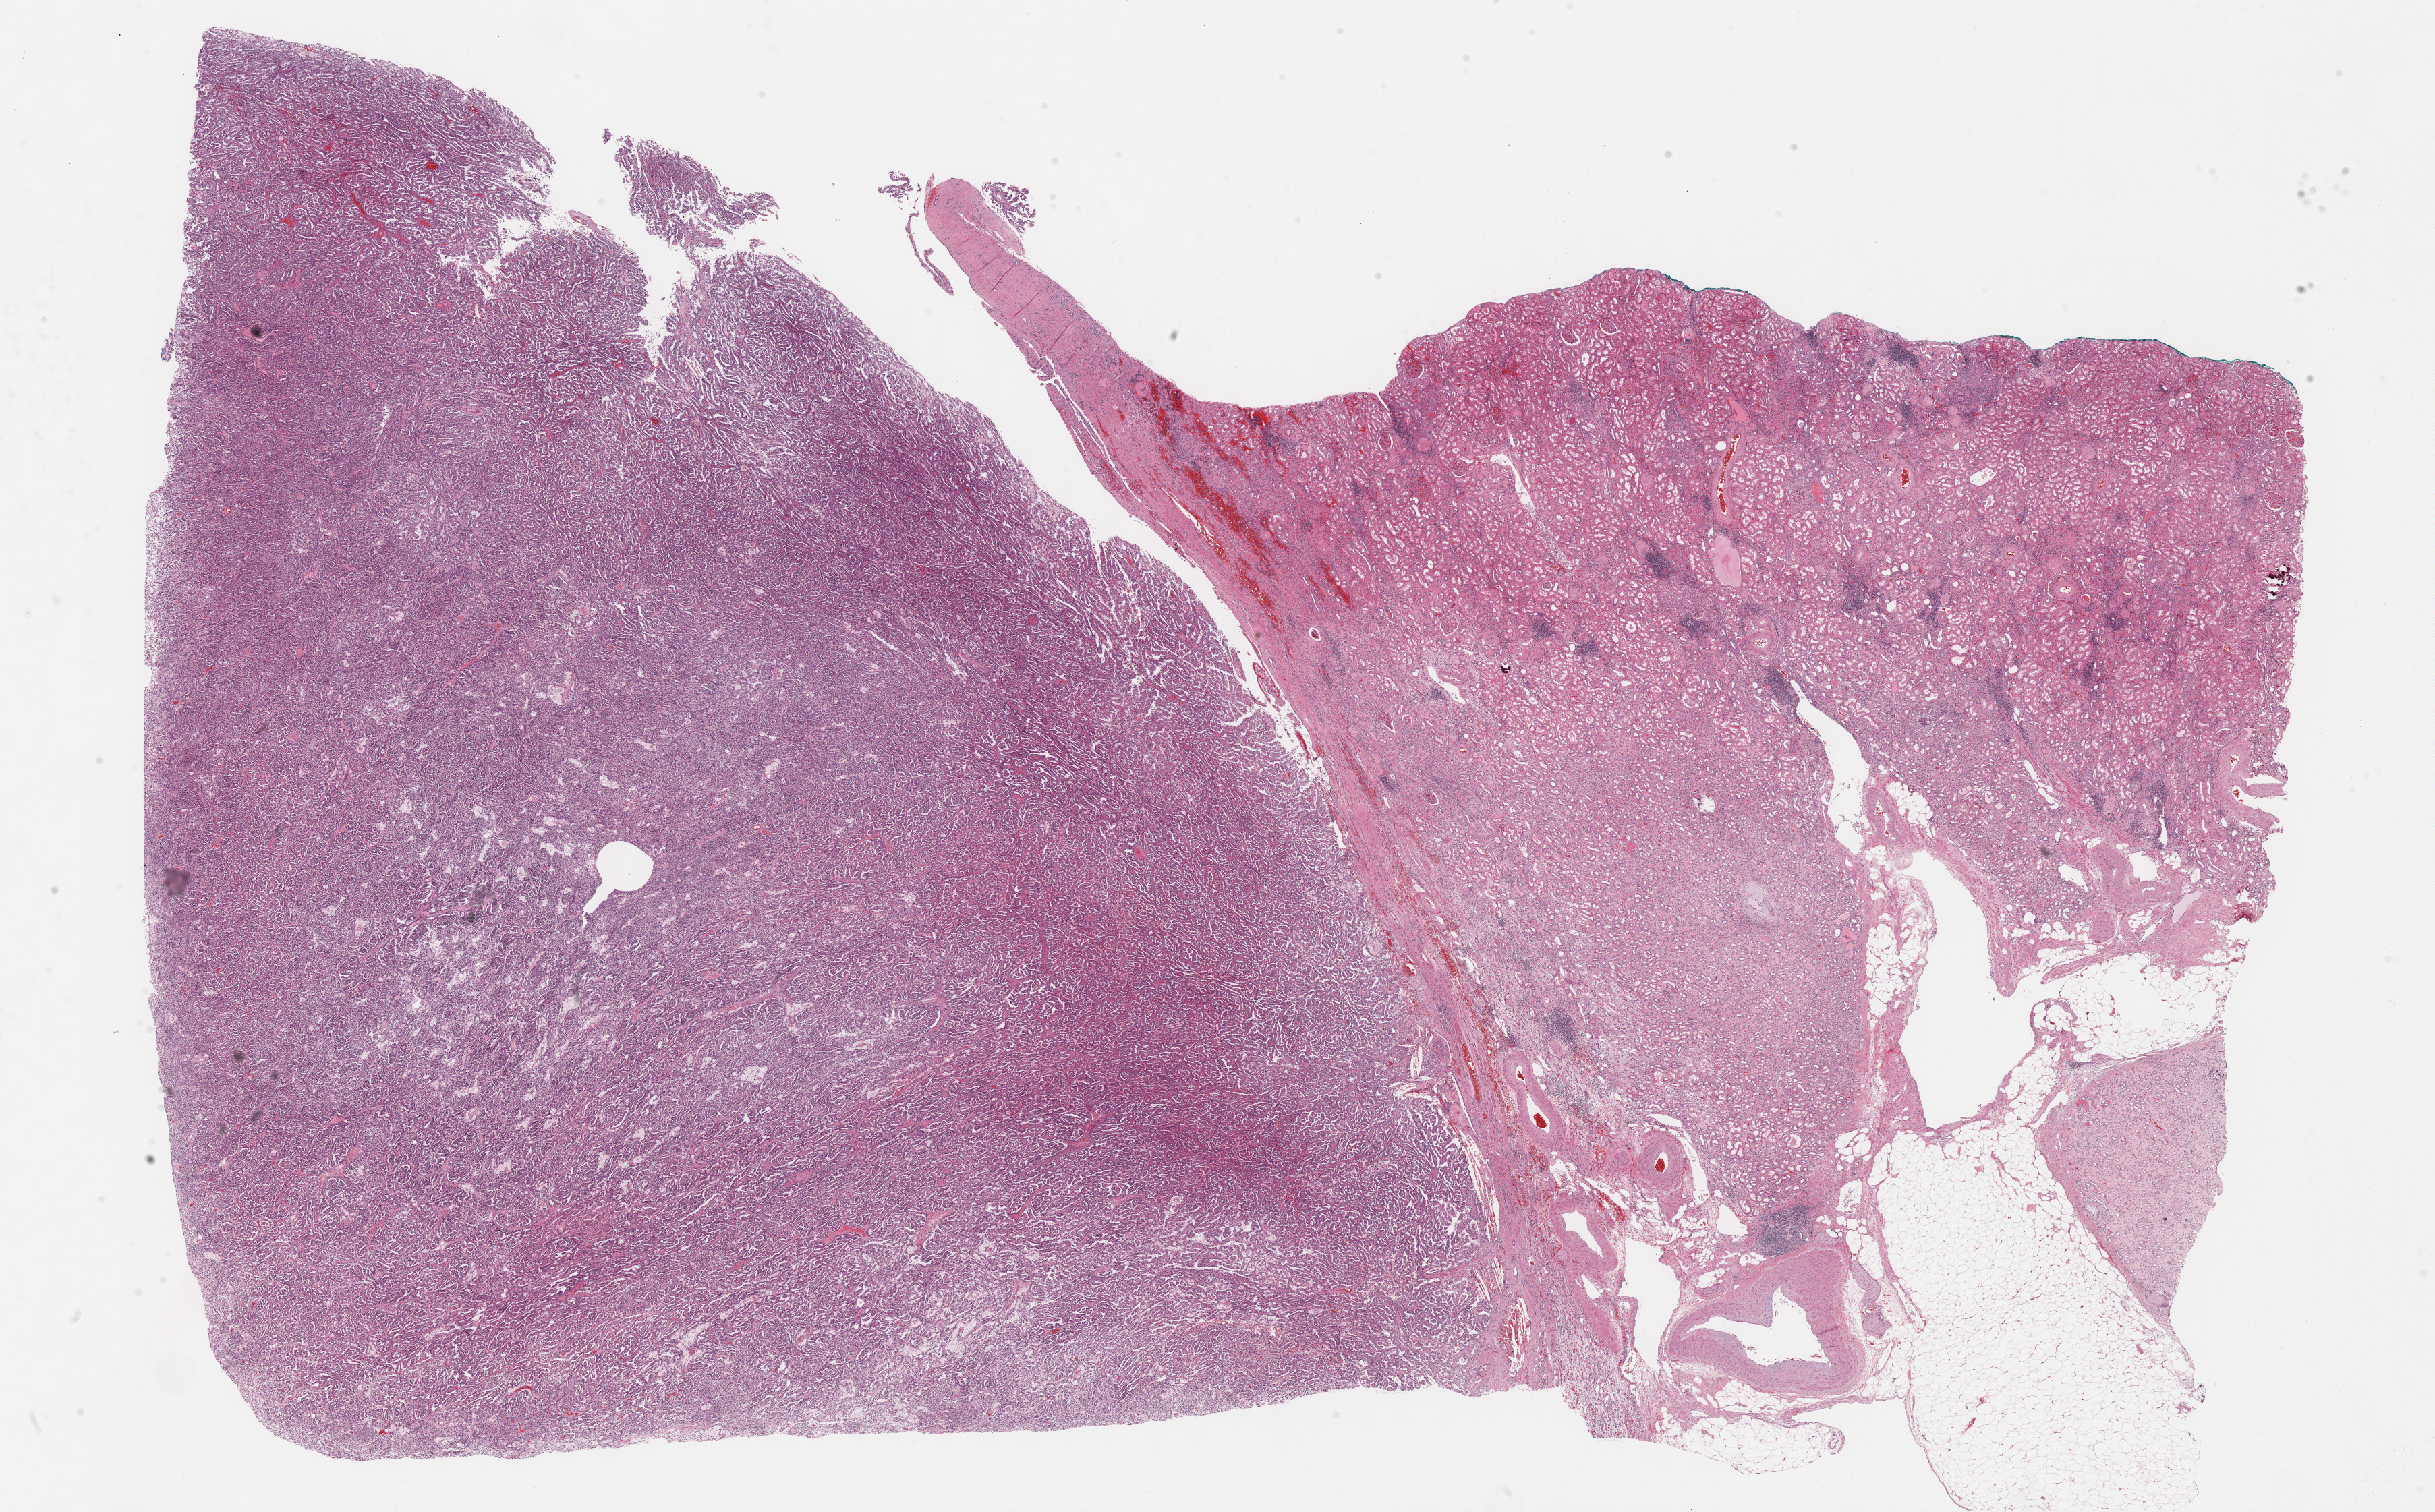
Digitized H&E-stained tissue section (whole slide), whole scanned area (about 29.2 x 18.1 mm, acquisition: 40x scan) shown as a low-resolution overview, formalin-fixed paraffin-embedded (FFPE) diagnostic section, sample: primary tumour, kidney. Male, age 74 years at initial diagnosis.
AJCC pathologic stage: I (7th edition). Histologic diagnosis: Papillary adenocarcinoma, NOS. TNM: T1b NX MX.